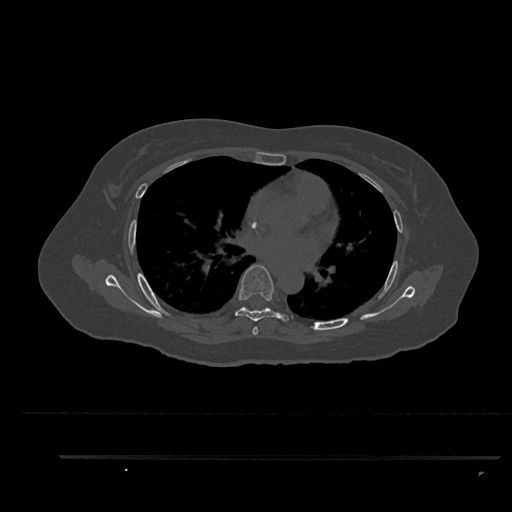
CT including the spine, one axial slice; slice 558 of 797 in the series (ordered by position); reconstruction kernel Br40s/3; 120 kVp; bone window (W 1800 / L 400 HU); 512 × 512 image matrix. Patient: female, 44 years. From the clinical record (not read from this slice): primary cancer: renal; vertebrae with lytic lesions (as recorded): L1.
Annotated regions visible in this slice (semi-automatic segmentation, software-assisted and operator-edited):
- T5 vertebra: box from (x=253, y=327) to (x=258, y=335) px
- T6 vertebra: (x=235, y=264)–(x=293, y=335)